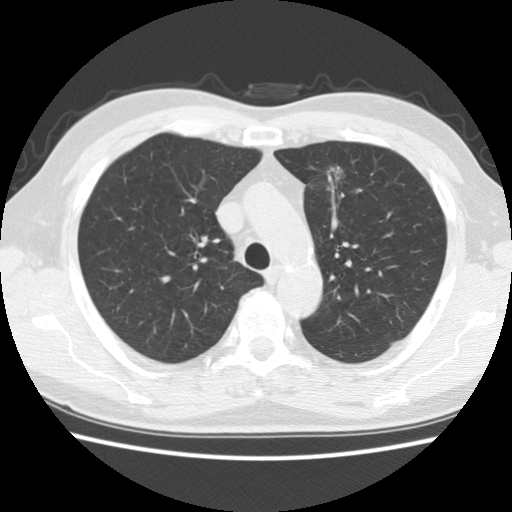
Axial slice from a low-dose chest CT screening exam, second screening round (one year after baseline), lung window (W 1500 / L -600 HU), 2.5 mm slice thickness, slice 49 of 172 in the series, 512 × 512 image matrix. Male participant, aged 63 years at enrolment.
- Expert reader's lesion annotation, box from (x=300, y=148) to (x=356, y=200) px.
- The exam's reader record, not a measurement of the box and not confirmed to be the same lesion: non-calcified nodule or mass ≥4 mm, left upper lobe, 23 × 18 mm, spiculated (stellate) margins, soft tissue attenuation, pre-existing on the prior screen: yes; interval growth: yes.